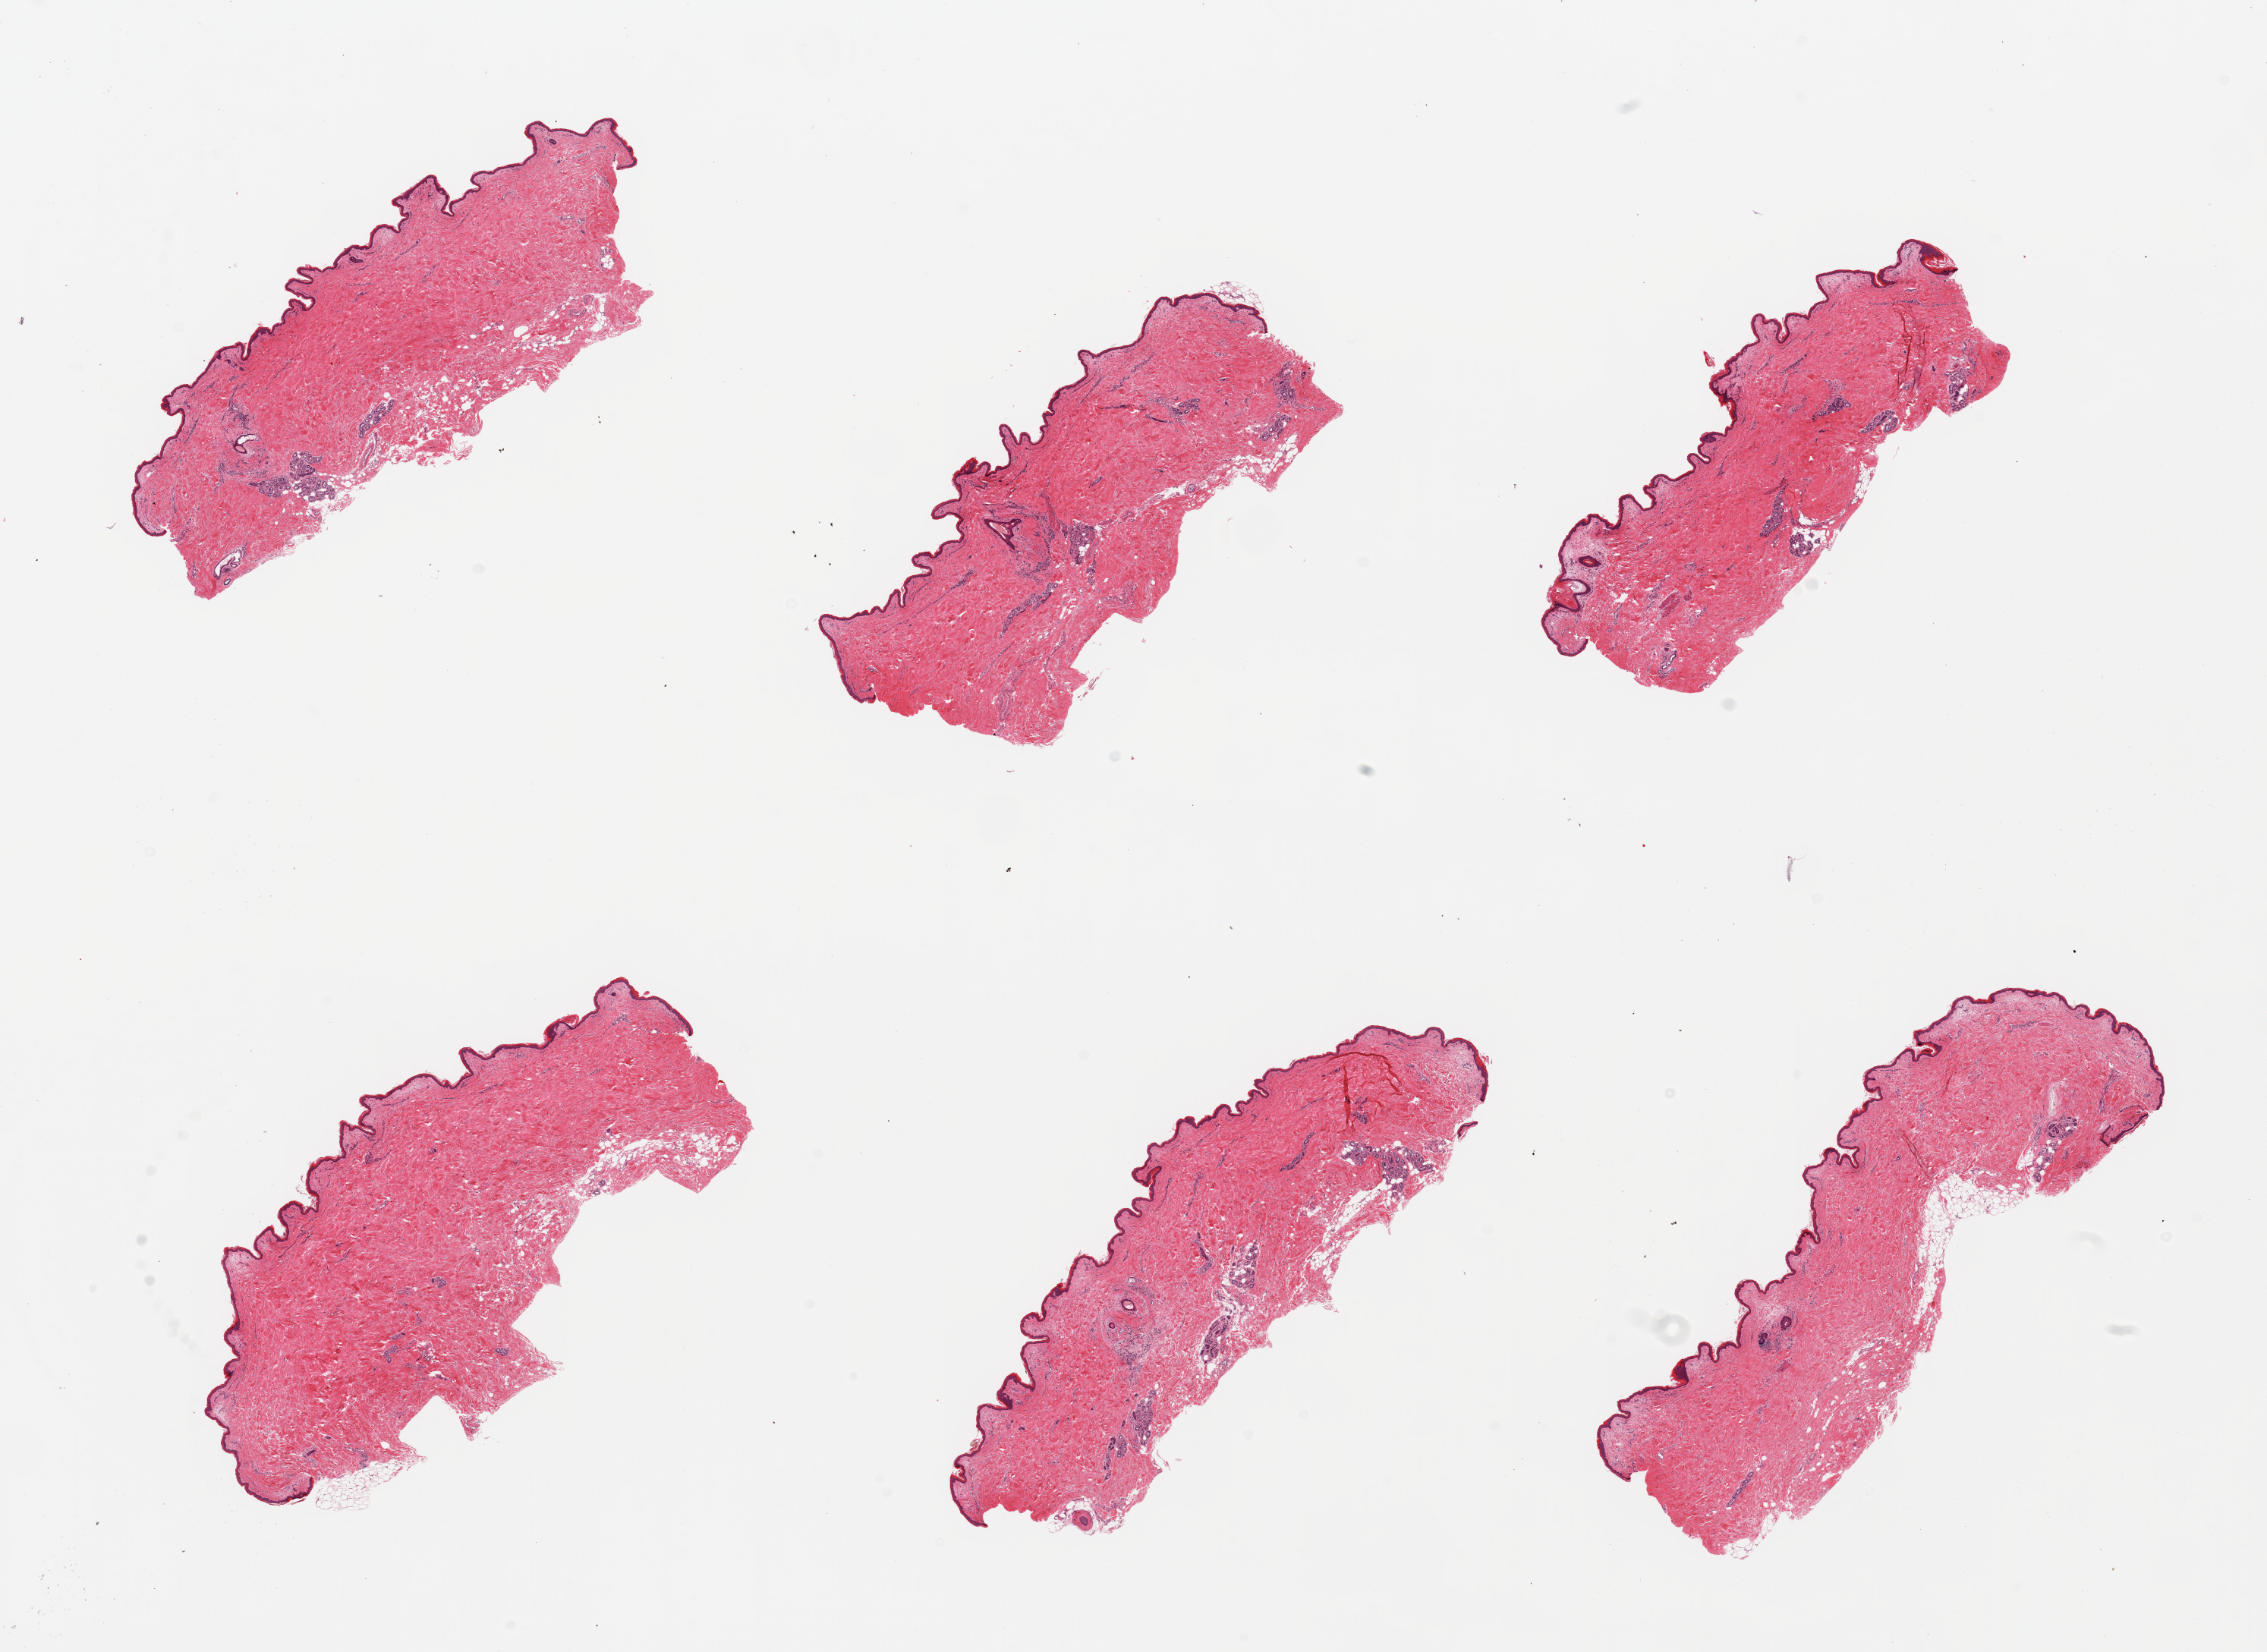
H&E whole-slide image, a low-resolution overview of the entire scanned area, about 23.6 x 17.2 mm (acquisition: 20x scan), PAXgene-fixed, paraffin-embedded tissue, section of skin of suprapubic region (target tissue), tissue donor sample. Donor sex: male.
Review note (as recorded): 6 pieces, atrophic squamous epithelium (~20-25 microns).